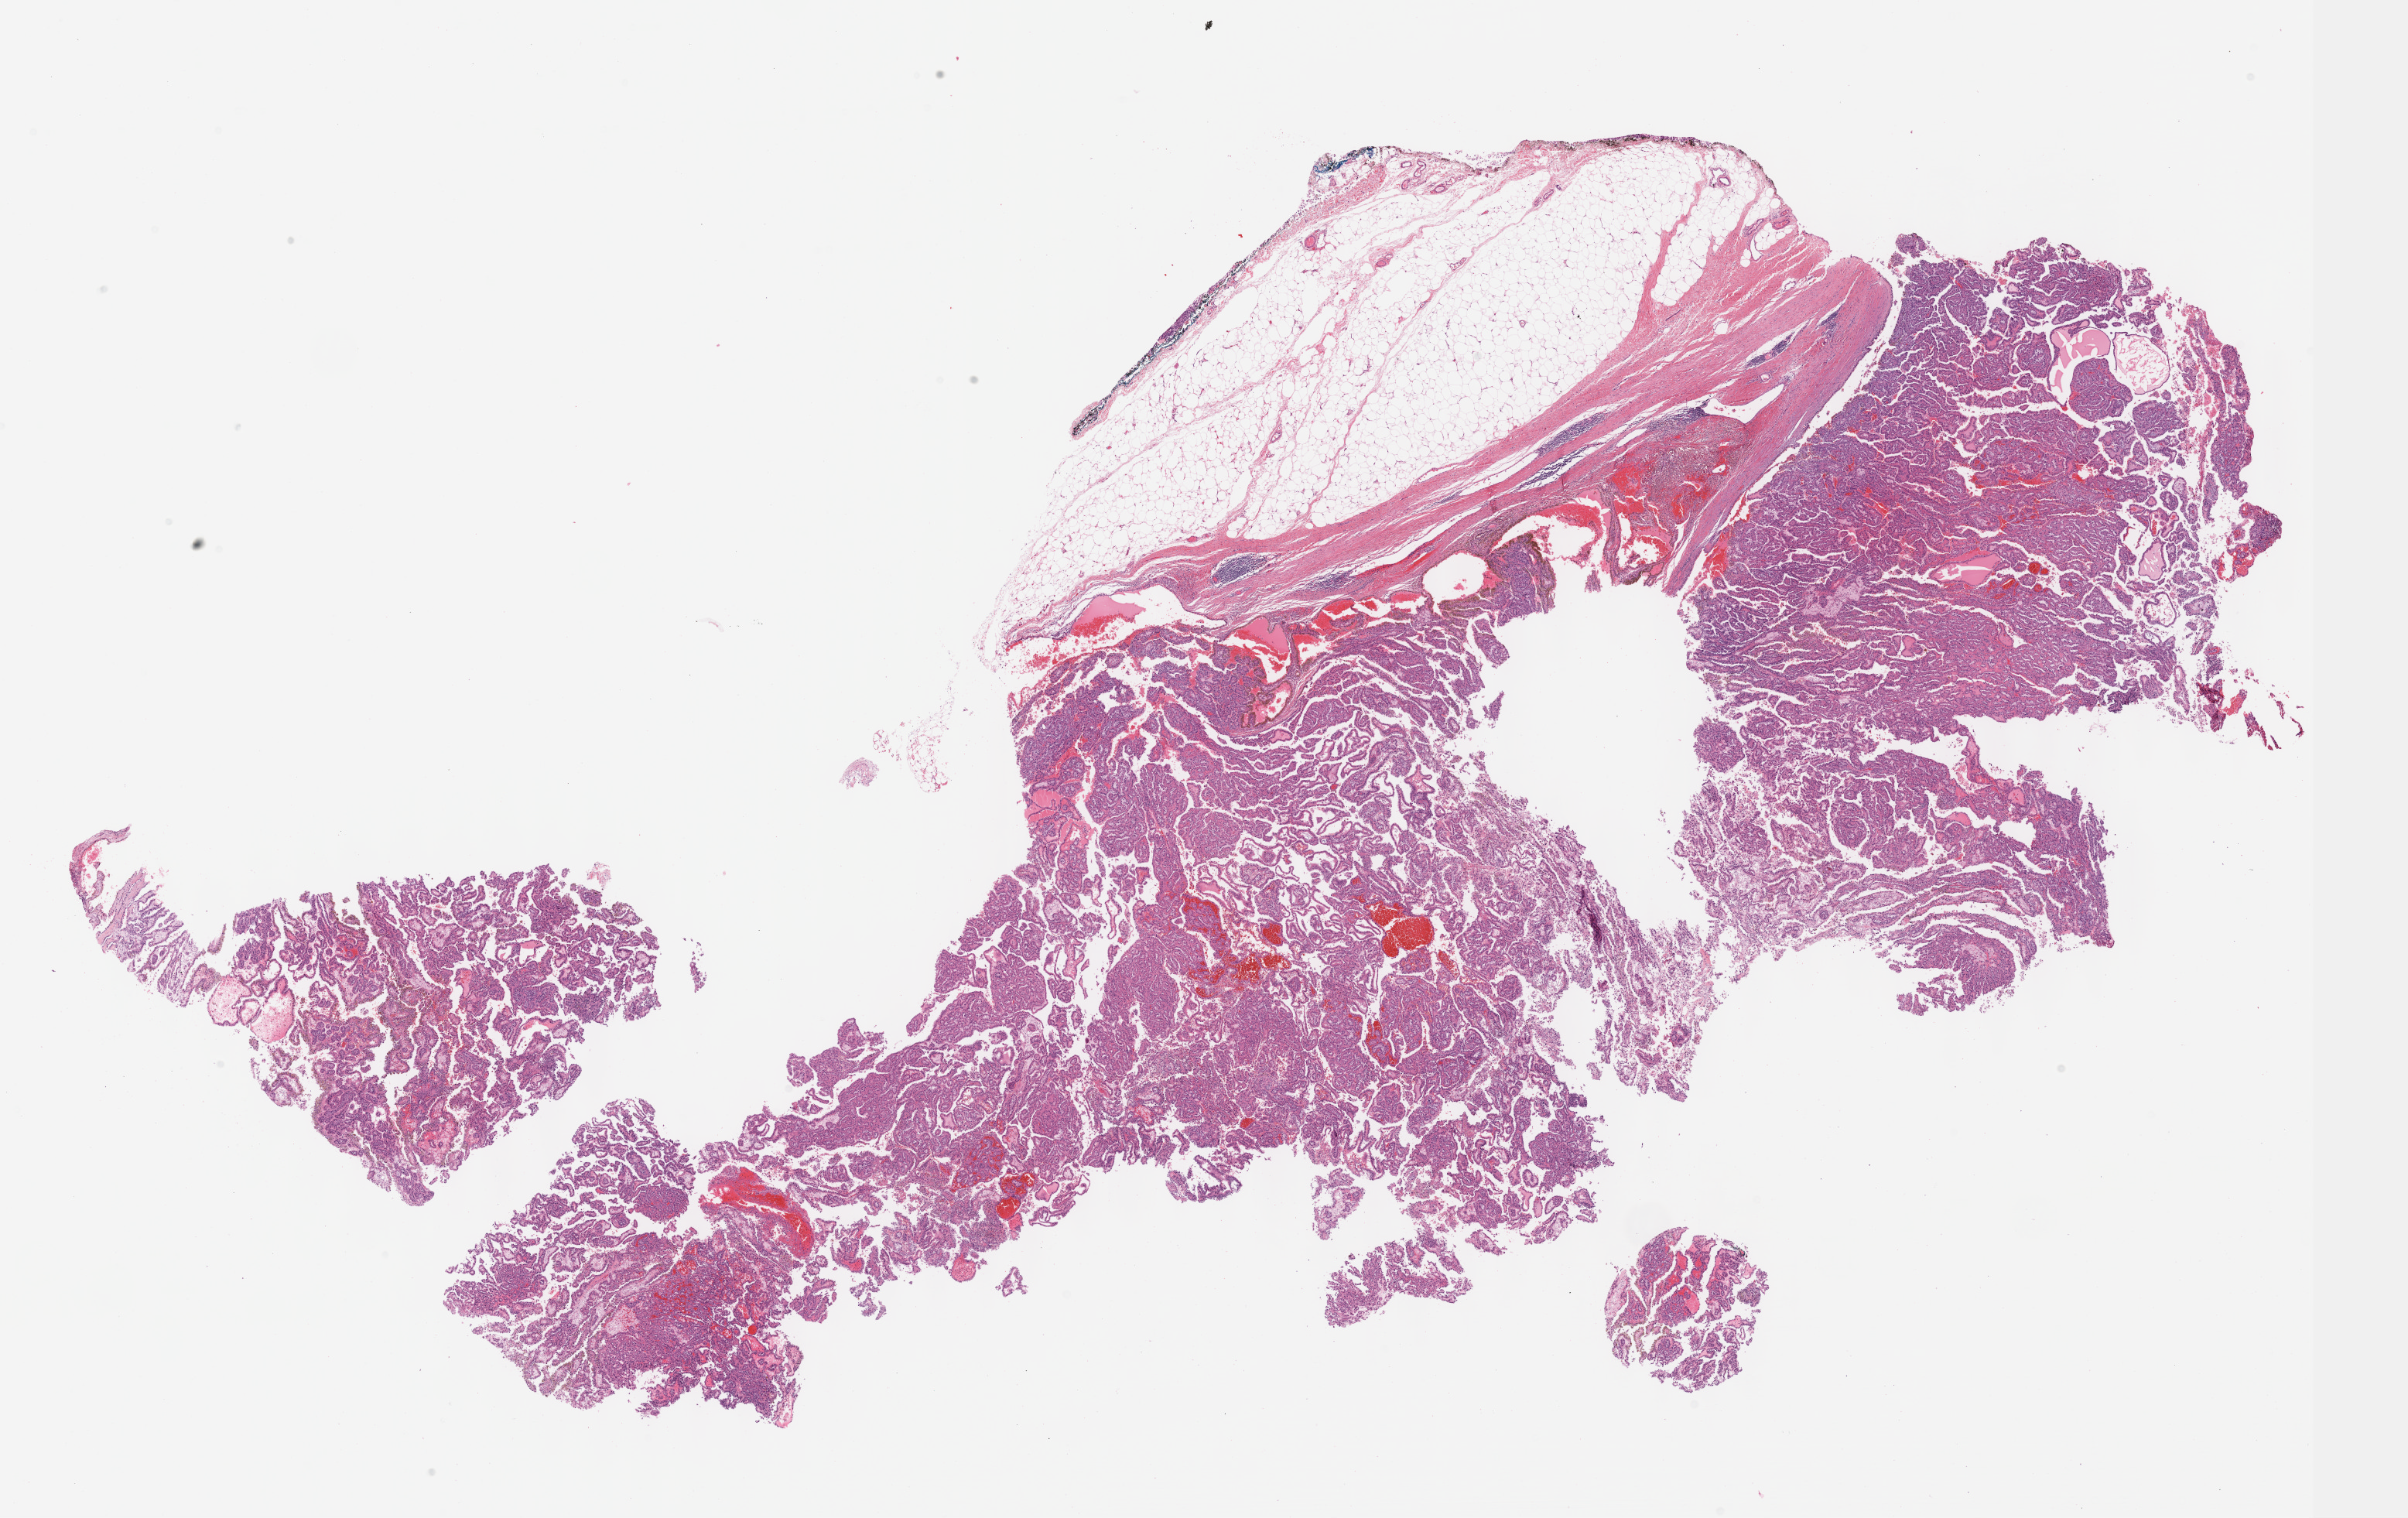
Whole-slide histology image, Hematoxylin and eosin (H&E) stained, shown as a low-resolution overview of the whole scanned area (about 25.1 x 15.9 mm, acquisition: 40x scan); formalin-fixed paraffin-embedded (FFPE) diagnostic section; kidney, primary tumour sample. Female patient; age at initial diagnosis 62 years.
AJCC pathologic stage: II (6th edition). Pathologic diagnosis: Papillary adenocarcinoma, NOS.